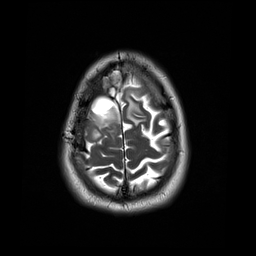
Brain MRI from a brain-tumour surgery series, one axial slice. Position 7 of 44 along the scan axis. 4 mm slice thickness. 256 × 256 image matrix, field of view 240 × 240 mm. Case-level facts recorded for this patient, not image findings: histopathology: Astrocytoma; WHO grade: 4; IDH mutation: yes; tumour location: Right Frontal.
Outlined on this slice (outlined manually by an expert reader):
- tumour: box from (x=88, y=107) to (x=120, y=146) px